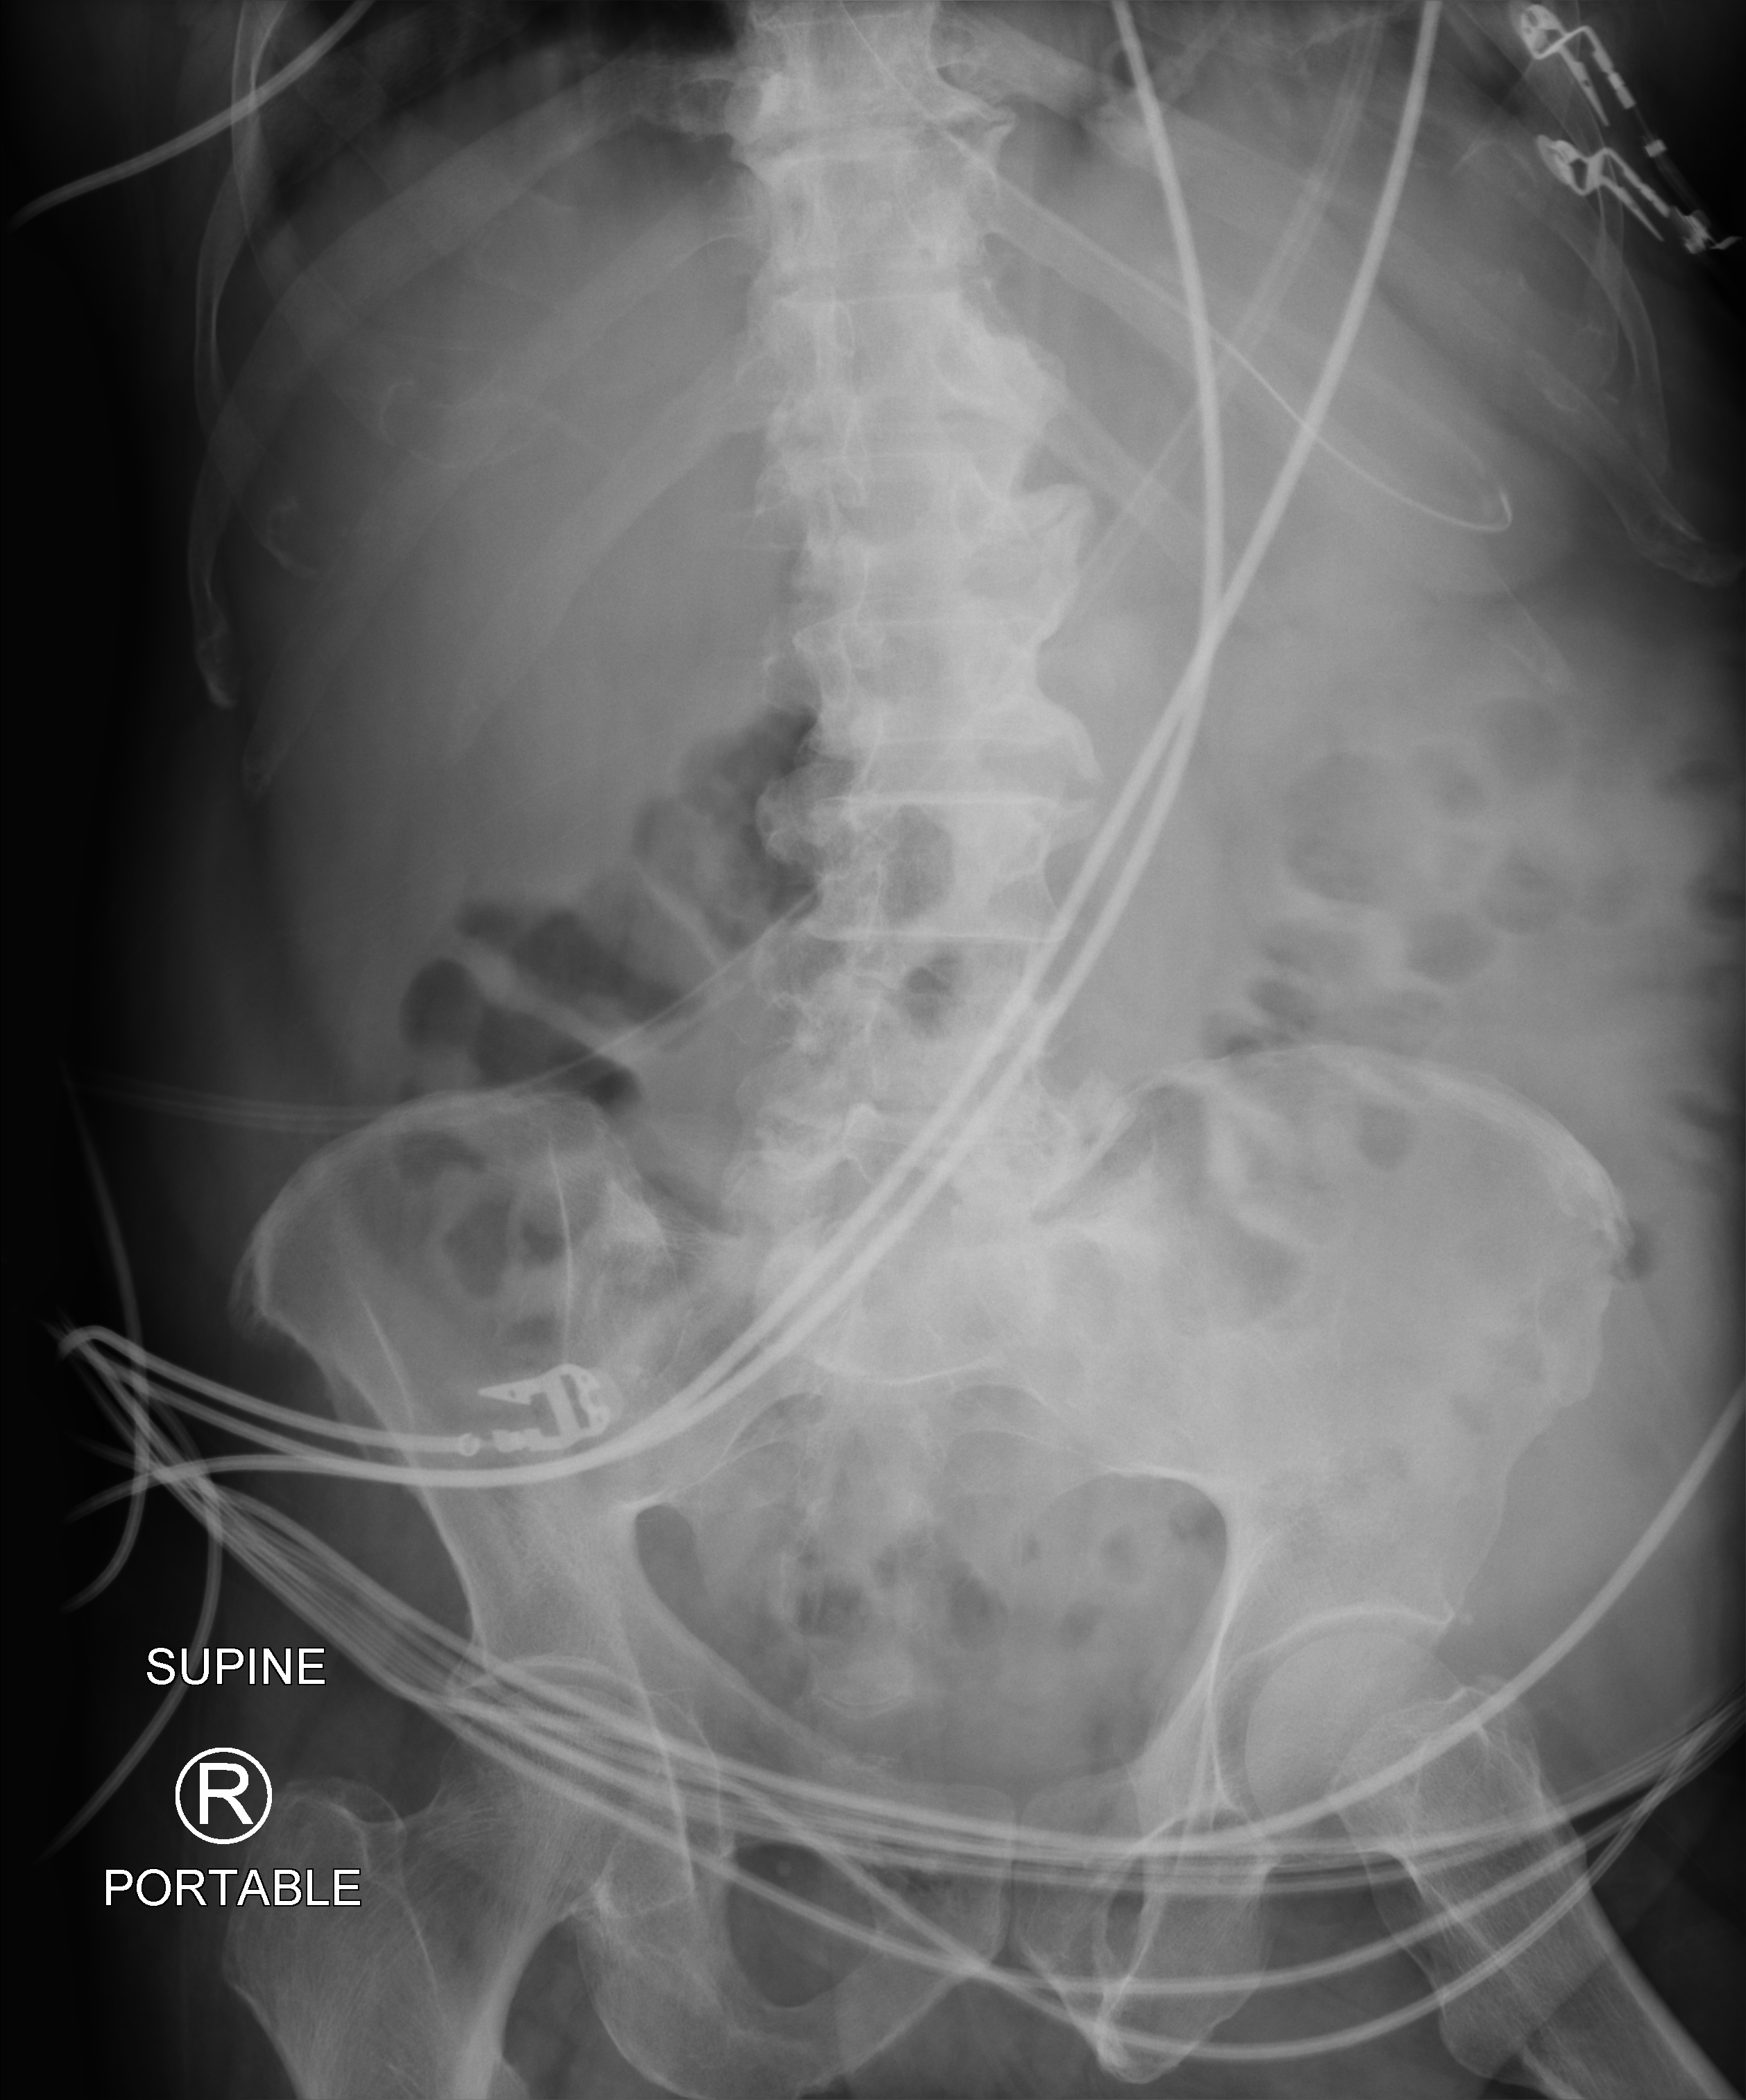
Abdomen X-ray (portable), anteroposterior (AP) projection. Patient hospitalised with COVID-19; male, aged 60–74 years.
Hospital-stay facts (about this admission, not read from this image; timing relative to this image not recorded):
- COPD (admission record): no
- mechanically ventilated during this hospital stay: yes